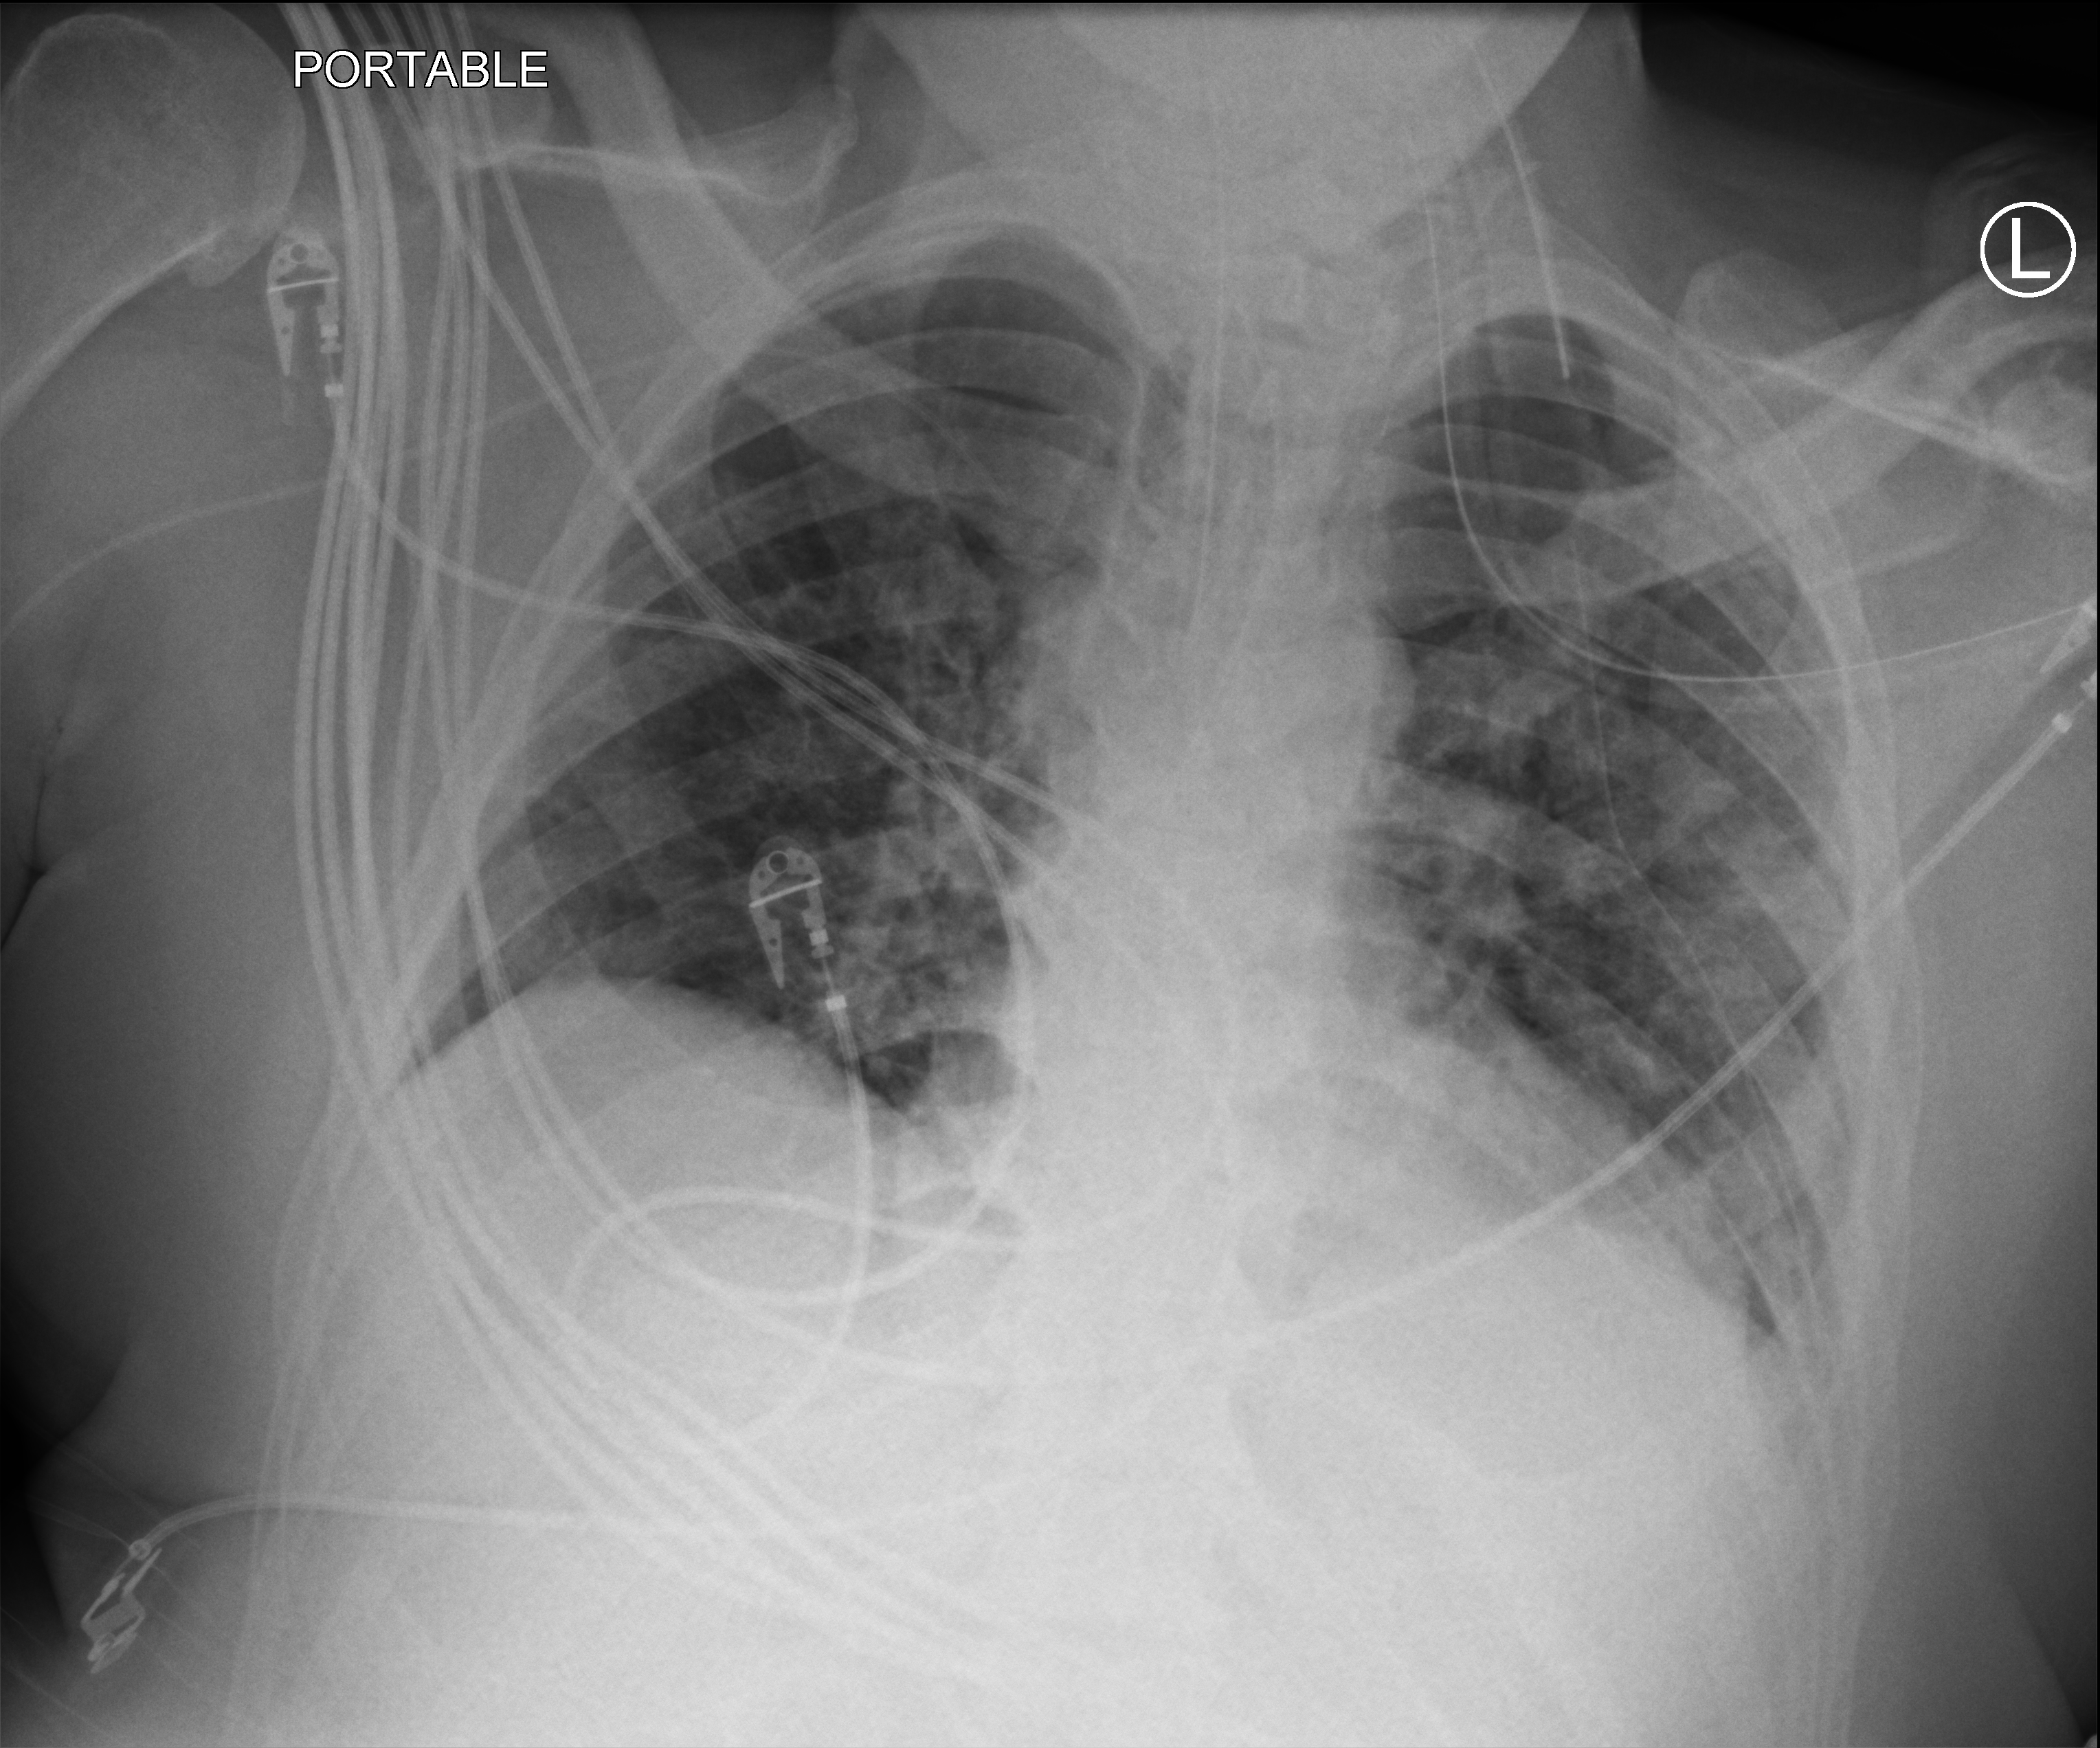
Bedside chest radiograph (computed radiography), anteroposterior (AP) projection. Patient hospitalised with COVID-19; male, aged 18–59 years.
Admission-level facts for this patient (not findings on this image; timing relative to this image not recorded): diabetes (admission record): no; hypertension (admission record): no.